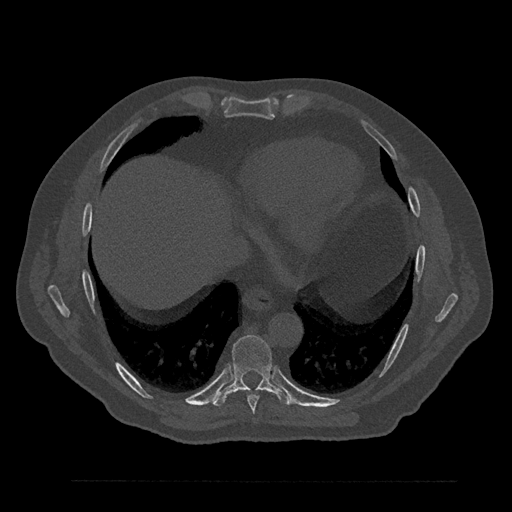
CT including the spine, one axial slice. Position 425 of 797 along the scan axis. Reconstruction kernel Br40s/3. Bone window (W 1800 / L 400 HU). 512 × 512 image matrix. Male patient, age 61 years. From the clinical record (not read from this slice): primary cancer: prostate.
Annotated regions visible in this slice (semi-automatic segmentation, software-assisted and operator-edited):
- T8 vertebra: bounding box <240,390,259,414> (left, top, right, bottom; pixels)
- T9 vertebra: <213,335,292,406>